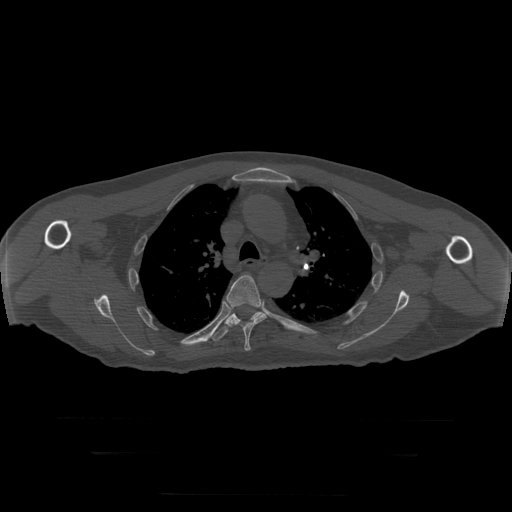
CT including the spine, one axial slice. Position 219 of 397 along the scan axis. Reconstruction kernel STANDARD. Bone window (W 1800 / L 400 HU). 1.25 mm slice thickness. 512 × 512 image matrix, field of view 510 × 510 mm. Patient age 73 years. From the clinical record (not read from this slice): primary cancer: prostate.
Annotated regions visible in this slice (semi-automatically segmented with operator editing):
- T5 vertebra: bounding box (x1, y1, x2, y2) in pixels: (227, 275, 267, 351)
- T6 vertebra: (208, 311, 264, 341)